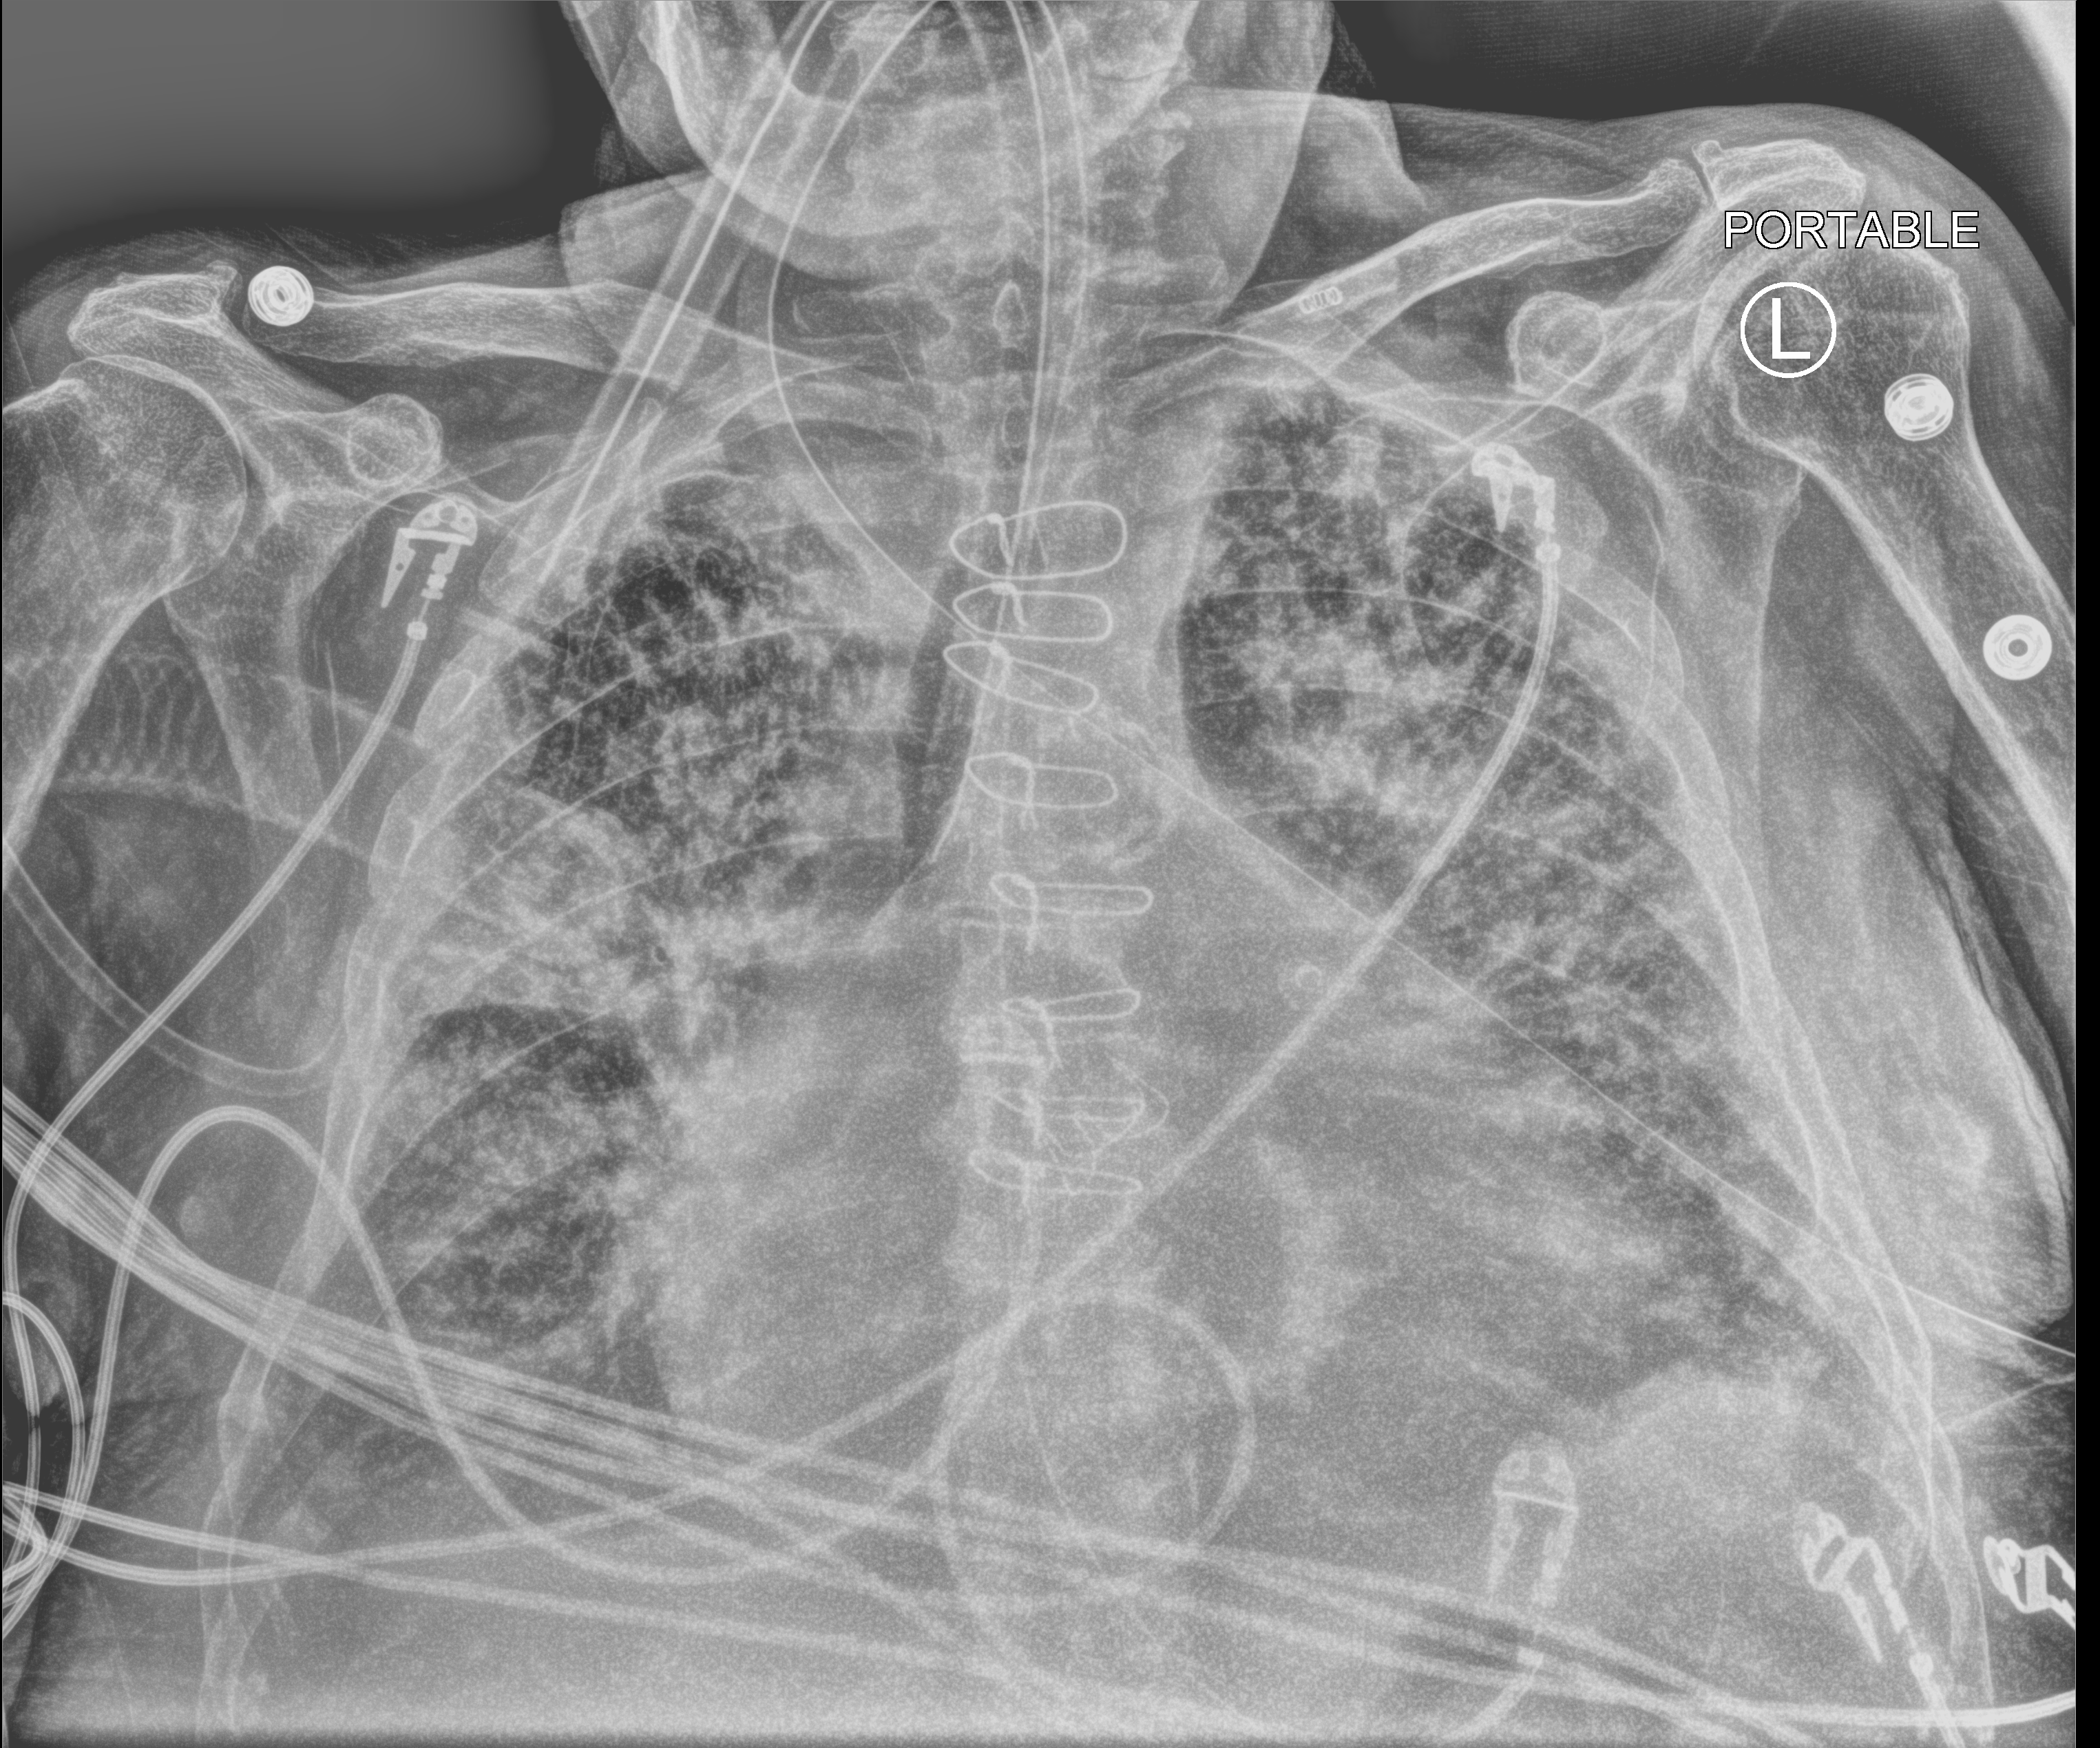
Chest X-ray (portable), anteroposterior (AP) projection. Patient hospitalised with COVID-19; male, aged 75–90 years.
Admission-level facts for this patient (not findings on this image; timing relative to this image not recorded):
- mechanically ventilated during this hospital stay: yes